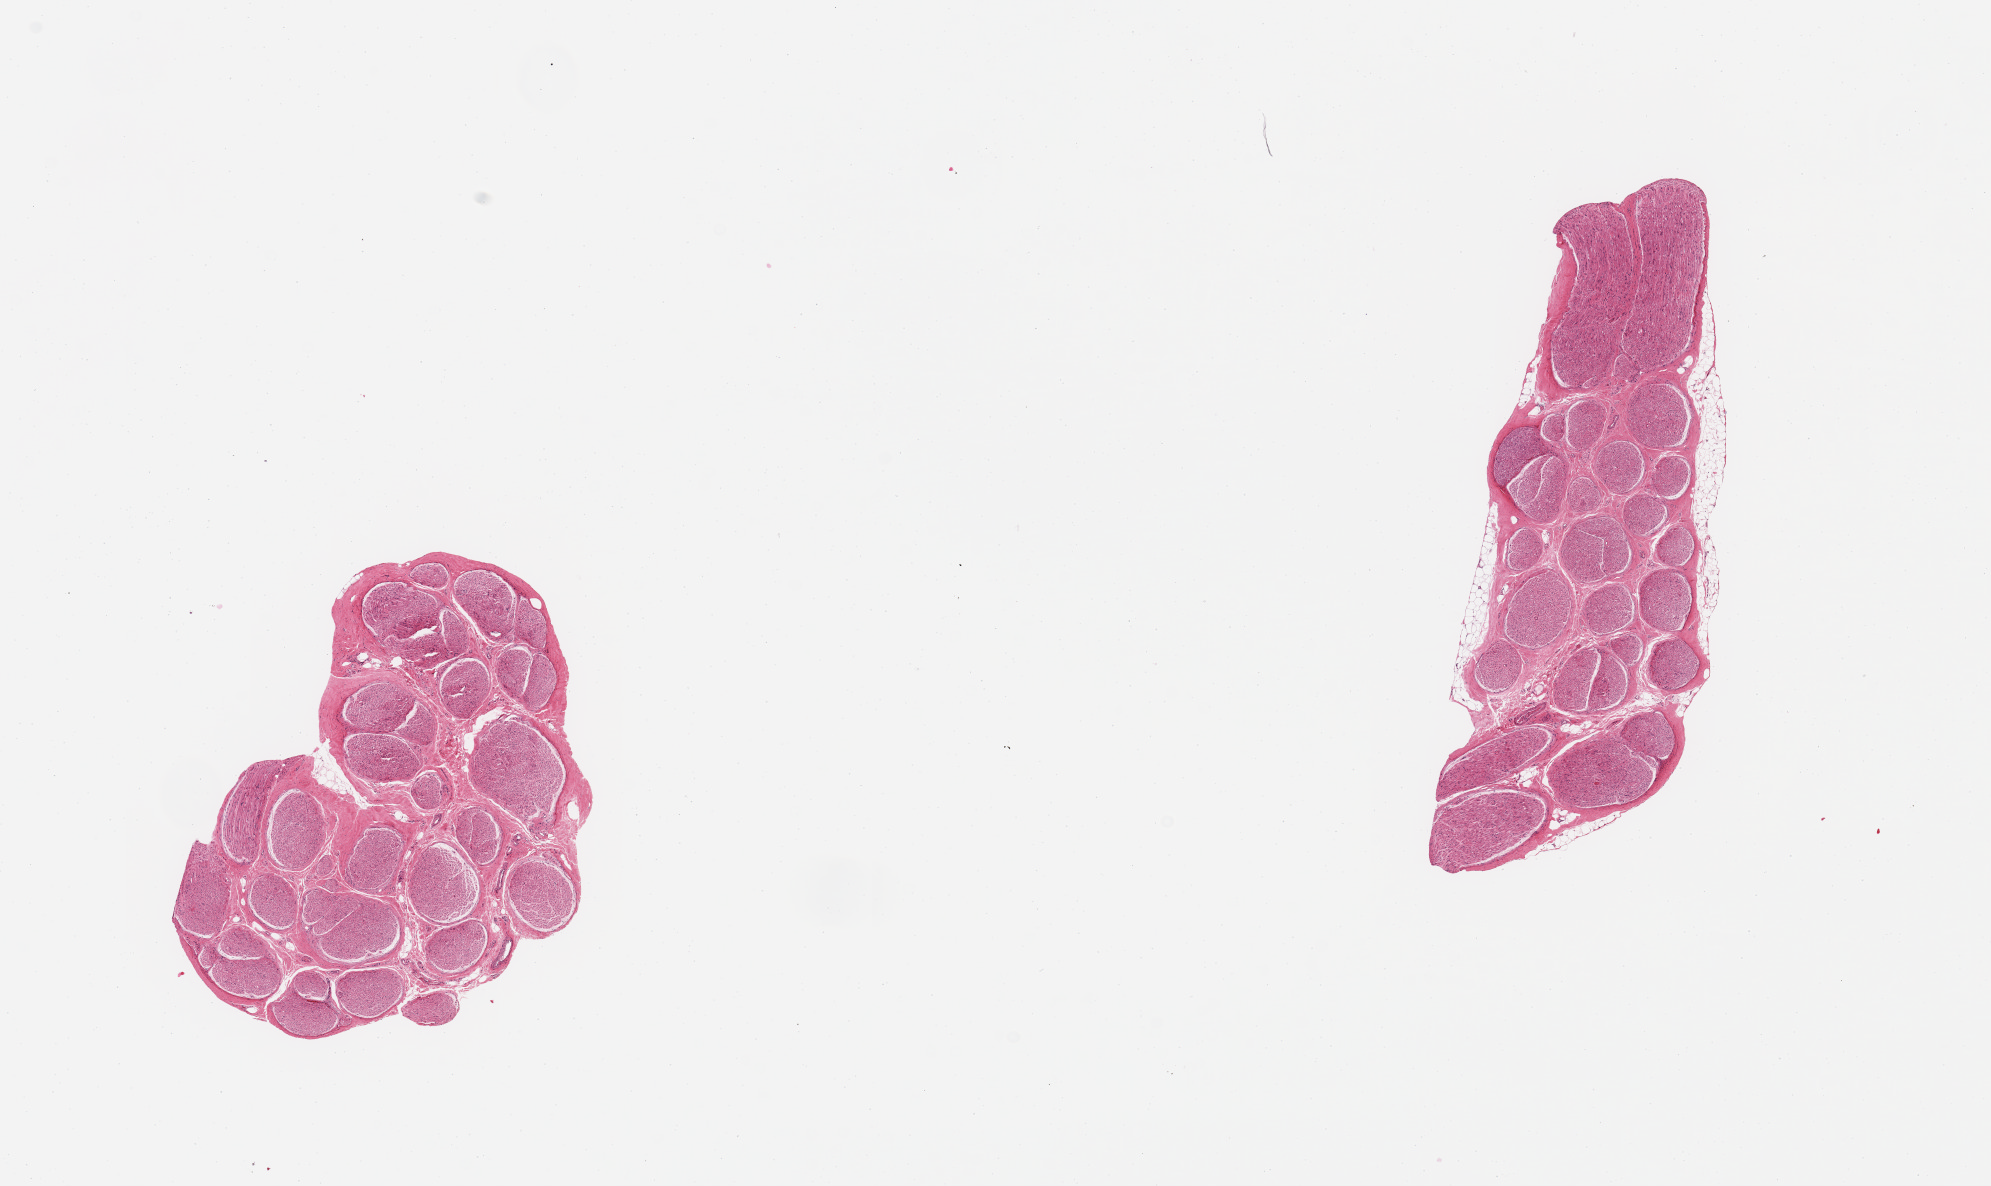
Digitized H&E-stained section — whole scanned area (about 15.8 x 9.4 mm) shown as a low-resolution overview; PAXgene-fixed, paraffin-embedded tissue; section of tibial nerve (target tissue); tissue donor sample. Donor: female.
* reviewer comment on this tissue sample: 2 pieces; <5% fat; well trimmed